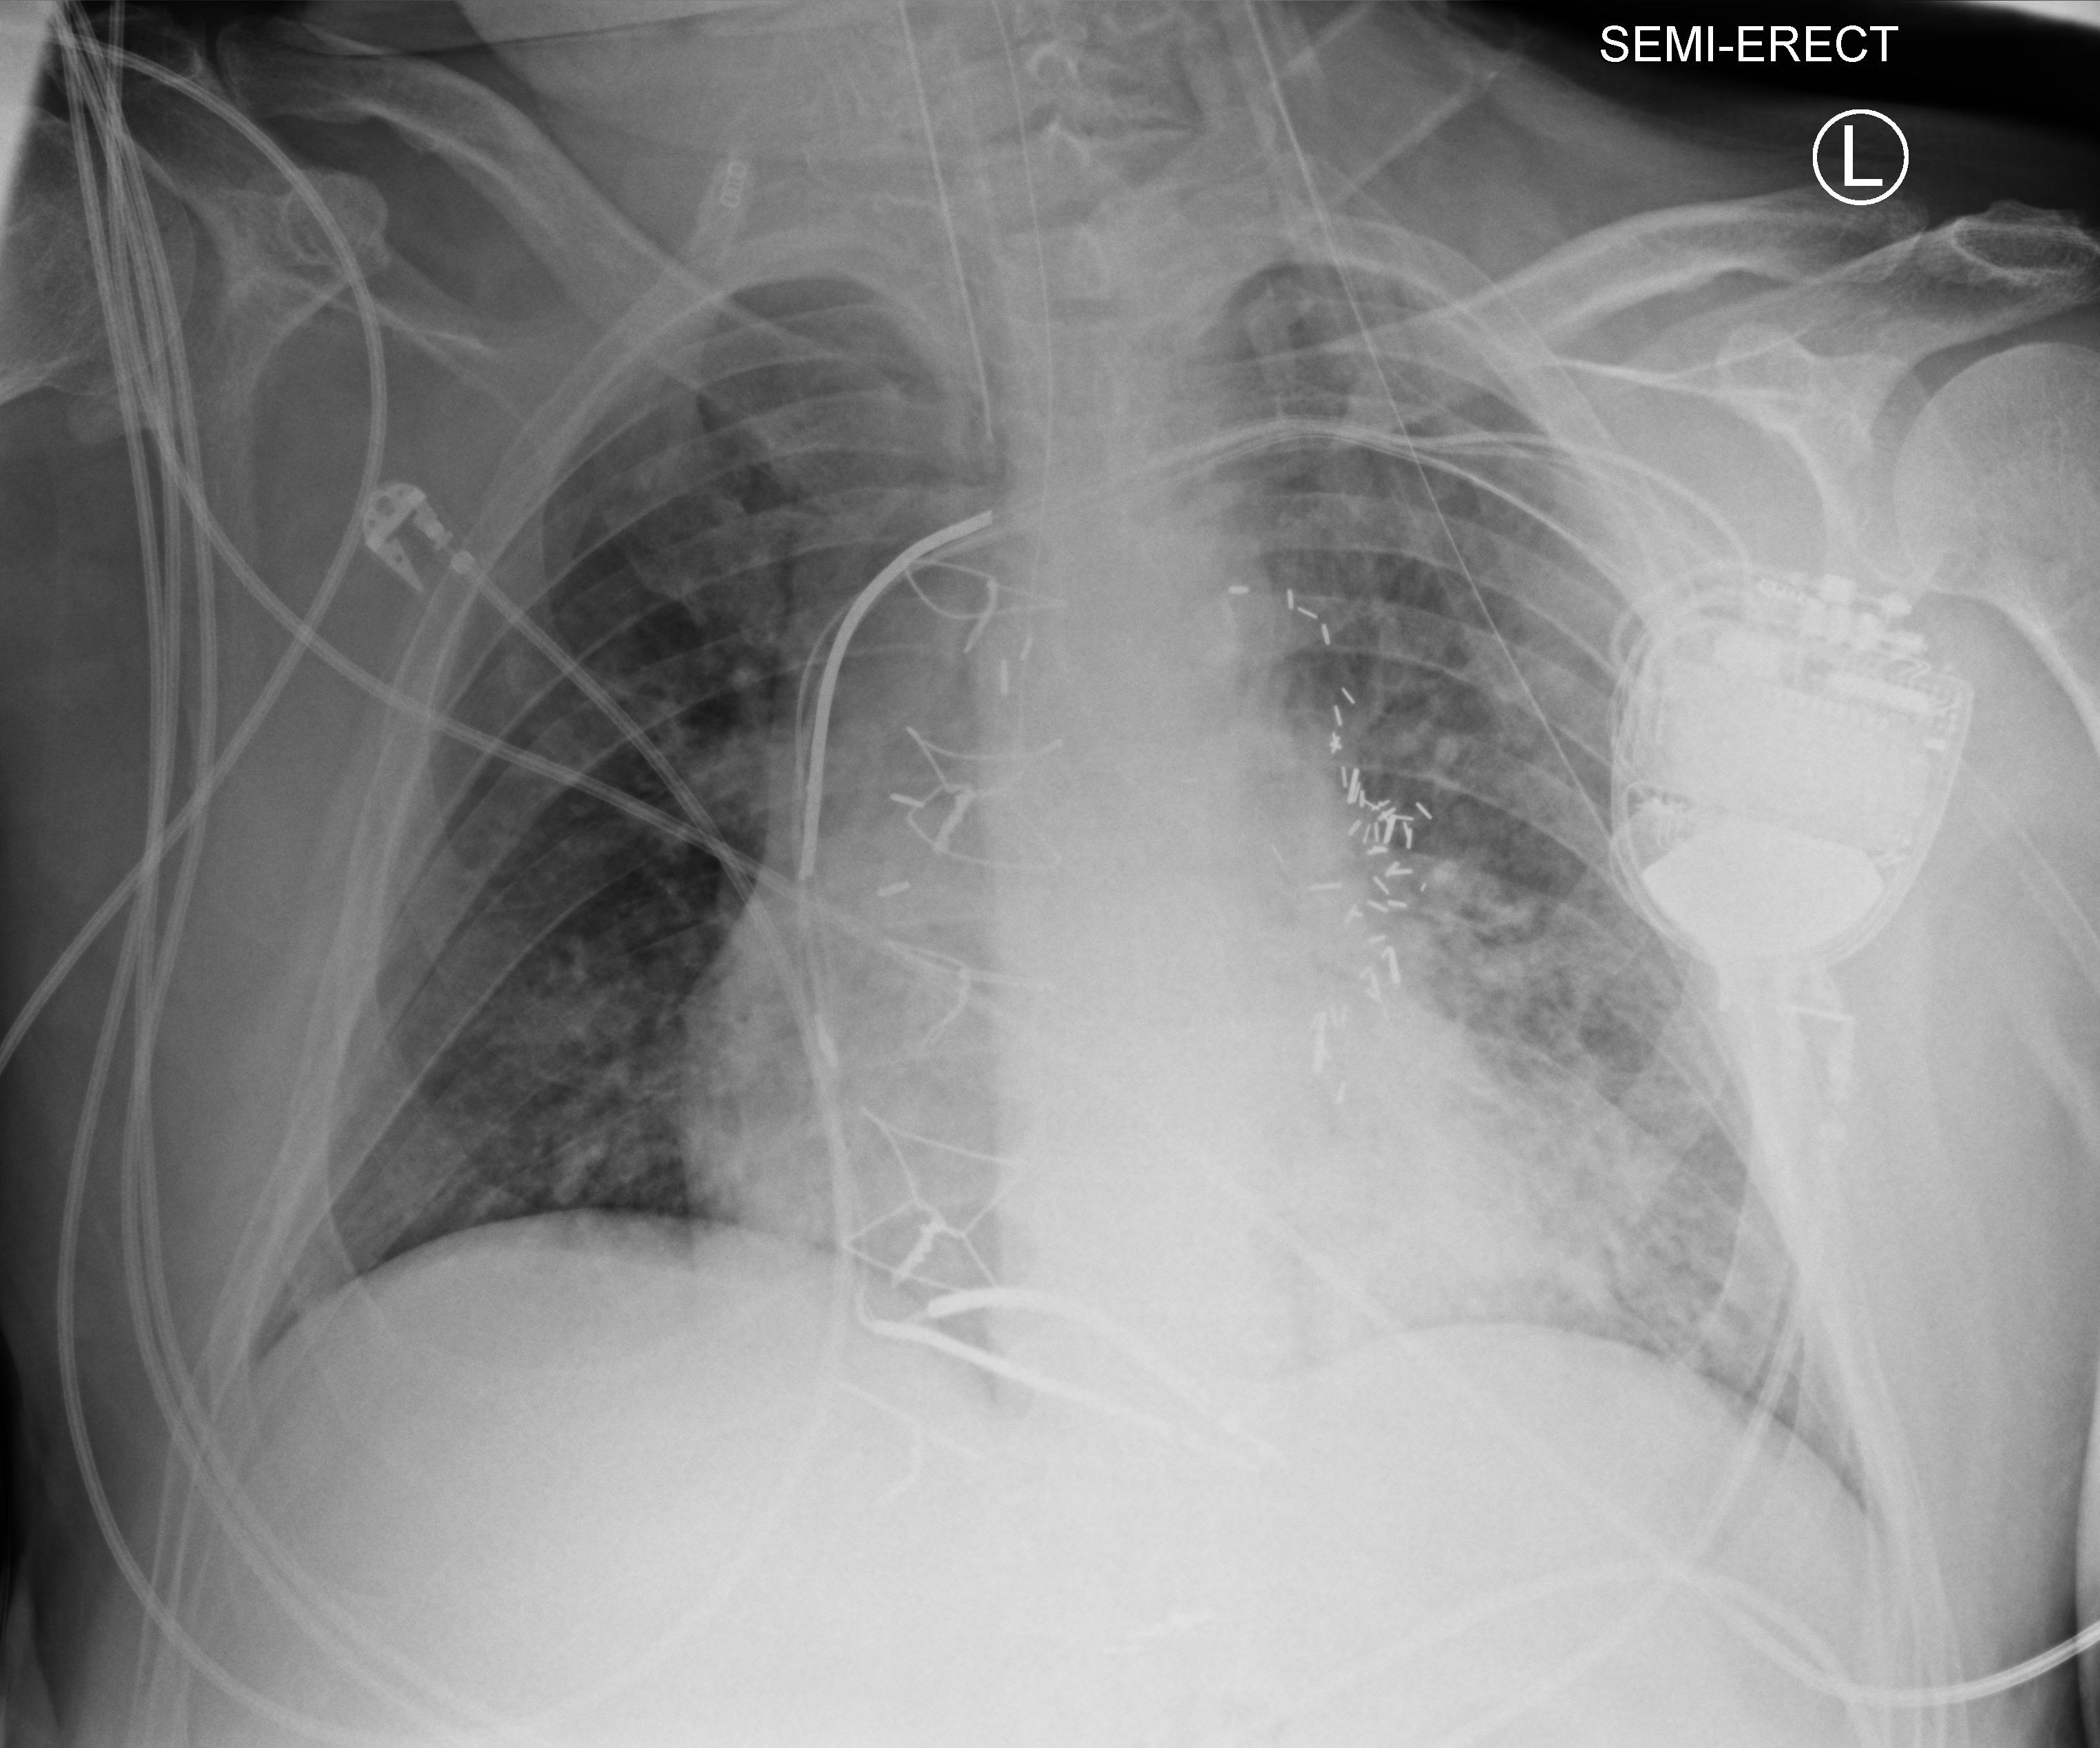
Portable chest radiograph; anteroposterior (AP) projection. Male patient hospitalised with COVID-19, age 60–74 years.
From the hospital-stay record, not from the radiograph (when in the stay this image was taken is not recorded): admitted to intensive care during this hospital stay: yes.